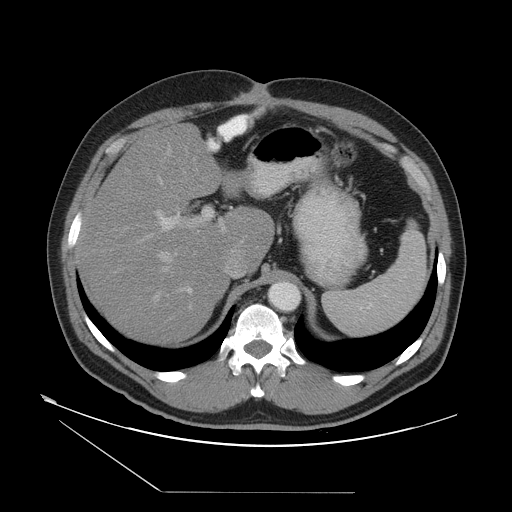
Contrast-enhanced abdominal CT, one axial slice. Intravenous contrast given. Soft-tissue window (W 400 / L 40 HU). 5 mm slice thickness. 512 × 512 image matrix. Male patient, age 59 years. From the clinical record (not read from this slice): diagnosis: colorectal cancer liver metastases, imaged before liver resection; multiple liver metastases: yes; largest metastasis: 0.3 cm; disease in both lobes: yes.
Structures marked on this image (outlined manually by an expert reader):
- hepatic veins: box from (x=153, y=178) to (x=196, y=302) px
- liver: (x=81, y=127)–(x=273, y=344)
- planned liver remnant (the part of the liver to remain after resection): (x=81, y=146)–(x=273, y=344)
- portal vein (with intrahepatic branches): (x=141, y=149)–(x=226, y=310)